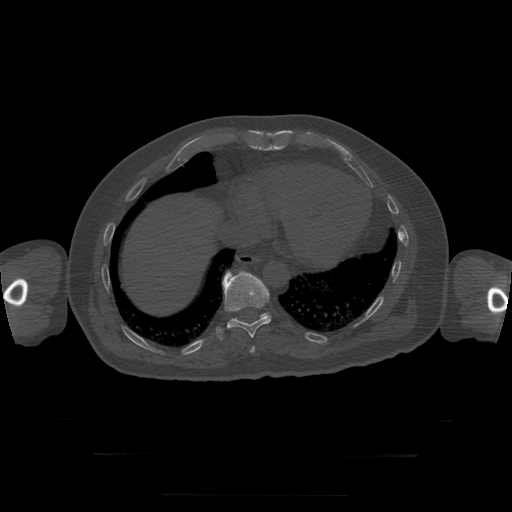
CT including the spine, one axial slice; slice 120 of 397 in the series (ordered by position); bone window (W 1800 / L 400 HU); 512 × 512 image matrix, field of view 510 × 510 mm. Patient age 73 years. Case-level facts recorded for this patient, not image findings: primary cancer: prostate.
Outlined on this slice (semi-automatically segmented with operator editing):
- T10 vertebra: box from (x=216, y=271) to (x=272, y=340) px
- T11 vertebra: (x=260, y=314)–(x=267, y=318)
- T9 vertebra: (x=250, y=347)–(x=255, y=353)